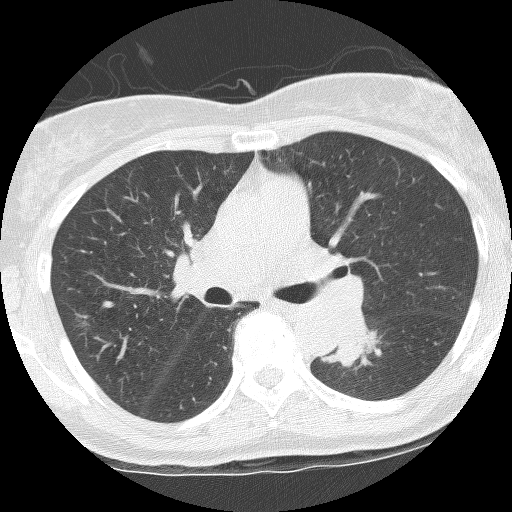
Chest CT (low-dose screening protocol), one axial image, third screening round (two years after baseline), lung window (W 1500 / L -600 HU), 2.5 mm slice thickness, slice 49 of 115 in the series. Female participant, aged 62 years at enrolment. Former smoker at enrolment.
- Expert reader's lesion annotation, bounding box <323,324,386,366> (left, top, right, bottom; pixels).
- The screening reader recorded 3 non-calcified nodules or masses ≥4 mm on this exam (right upper lobe, left lower lobe, left upper lobe); which of them this box marks is not recorded.
- Official screen result: positive, other.
- Later outcome: lung cancer diagnosed 165 days after this screen — squamous cell carcinoma, NOS, left lower lobe, stage IIIB (AJCC 6th edition), 31 mm at pathology.